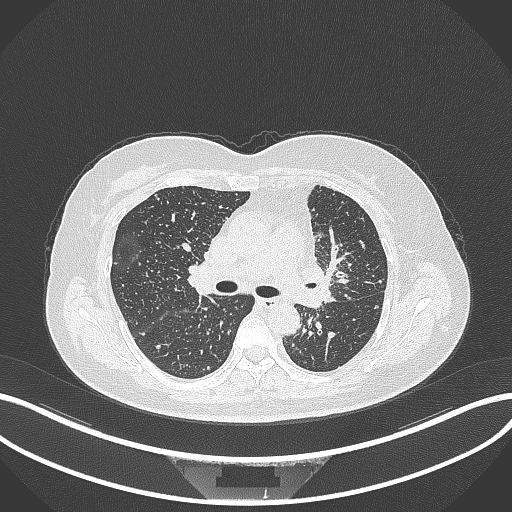
Chest CT, one axial slice; position 205 of 348 along the scan axis; lung window (W 1500 / L -600 HU); 1 mm slice thickness; 512 × 512 image matrix, field of view 400 × 400 mm. Female patient, age 49 years. Case-level facts recorded for this patient, not image findings: clinical TNM (as recorded): T1c N0 M1.
Outlined on this slice (rectangle marked by the reading radiologist):
- lung tumour (recorded histology: adenocarcinoma): bounding box <291,258,346,314> (left, top, right, bottom; pixels)